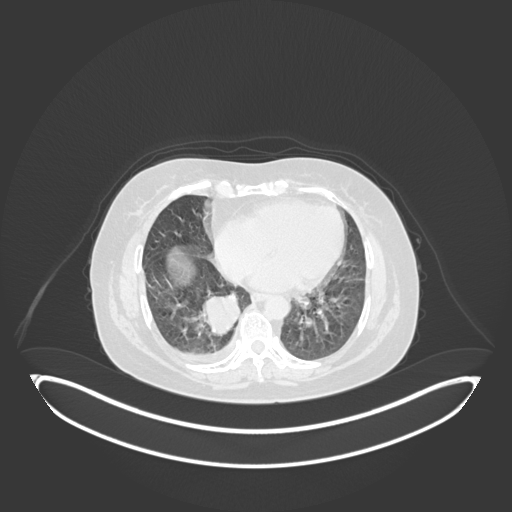
Chest CT, one axial slice; 120 kVp; lung window (W 1500 / L -600 HU); 1 mm slice thickness; 512 × 512 image matrix, field of view 500 × 500 mm. Patient: female, 56 years. Case-level facts recorded for this patient, not image findings: clinical TNM (as recorded): T2b N1 M0; histopathological grade: G3.
Outlined on this slice (bounding box drawn by a radiologist):
- lung tumour (recorded histology: small cell carcinoma): box from (x=199, y=286) to (x=245, y=340) px